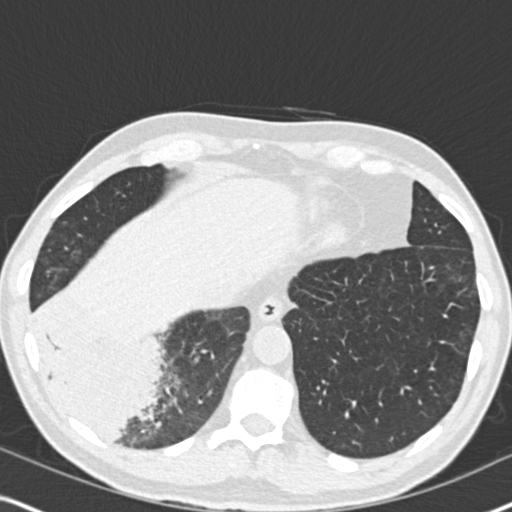
Axial slice from a low-dose chest CT screening exam. Second annual screen. Lung window (W 1500 / L -600 HU). 2 mm slice thickness. 120 kVp. Male participant, aged 61 years at enrolment. Current smoker at enrolment.
- Lesion marked by an expert reader, box from (x=23, y=286) to (x=181, y=456) px.
- Screening reader's record for this exam (one nodule recorded; not confirmed to be the boxed lesion): non-calcified nodule or mass ≥4 mm, right lower lobe, 90 × 80 mm, soft tissue attenuation, pre-existing on the prior screen: yes; interval growth: yes.
- Participant outcome: lung cancer diagnosed 20 days after this screen — bronchiolo-alveolar adenocarcinoma, NOS, right lower lobe, moderately differentiated (G2), stage IIIB (AJCC 6th edition), 90 mm at pathology.